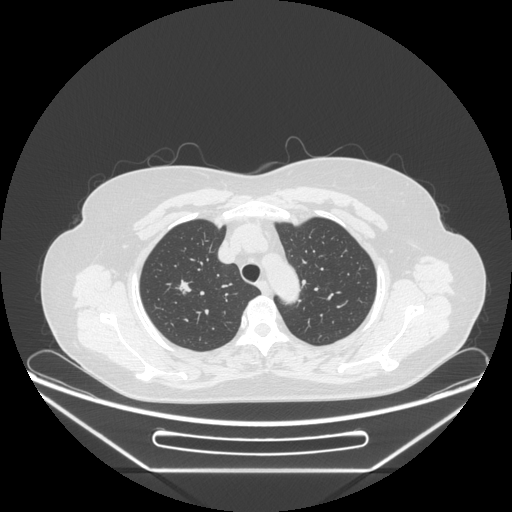
Chest CT, one axial slice. Position 195 of 236 along the scan axis. 120 kVp. Lung window (W 1500 / L -600 HU). 1.25 mm slice thickness. 512 × 512 image matrix. Female patient, age 60 years. From the clinical record (not read from this slice): clinical TNM (as recorded): T1c N0 M0.
Outlined on this slice (rectangle marked by the reading radiologist):
- lung tumour (recorded histology: adenocarcinoma): bounding box <168,268,202,304> (left, top, right, bottom; pixels)